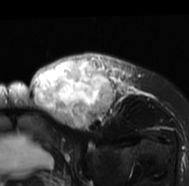
MRI of an extremity soft-tissue mass, one axial slice; slice 47 of 77 in the series (ordered by position); T2-weighted fat-saturated; MR volume resampled by the dataset authors to the PET/CT grid (not the native acquisition matrix); 3.27 mm slice thickness; 189 × 186 image matrix, field of view 185 × 182 mm. Female patient. From the clinical record (not read from this slice): histological type: leiomyosarcoma; grade: high; site of the primary tumour: groin.
Annotated regions visible in this slice (expert contour drawn on MRI and transferred to this co-registered scan by the dataset authors):
- gross tumour volume including surrounding oedema: box from (x=28, y=52) to (x=153, y=130) px
- gross tumour volume (mass): (x=29, y=56)–(x=114, y=130)